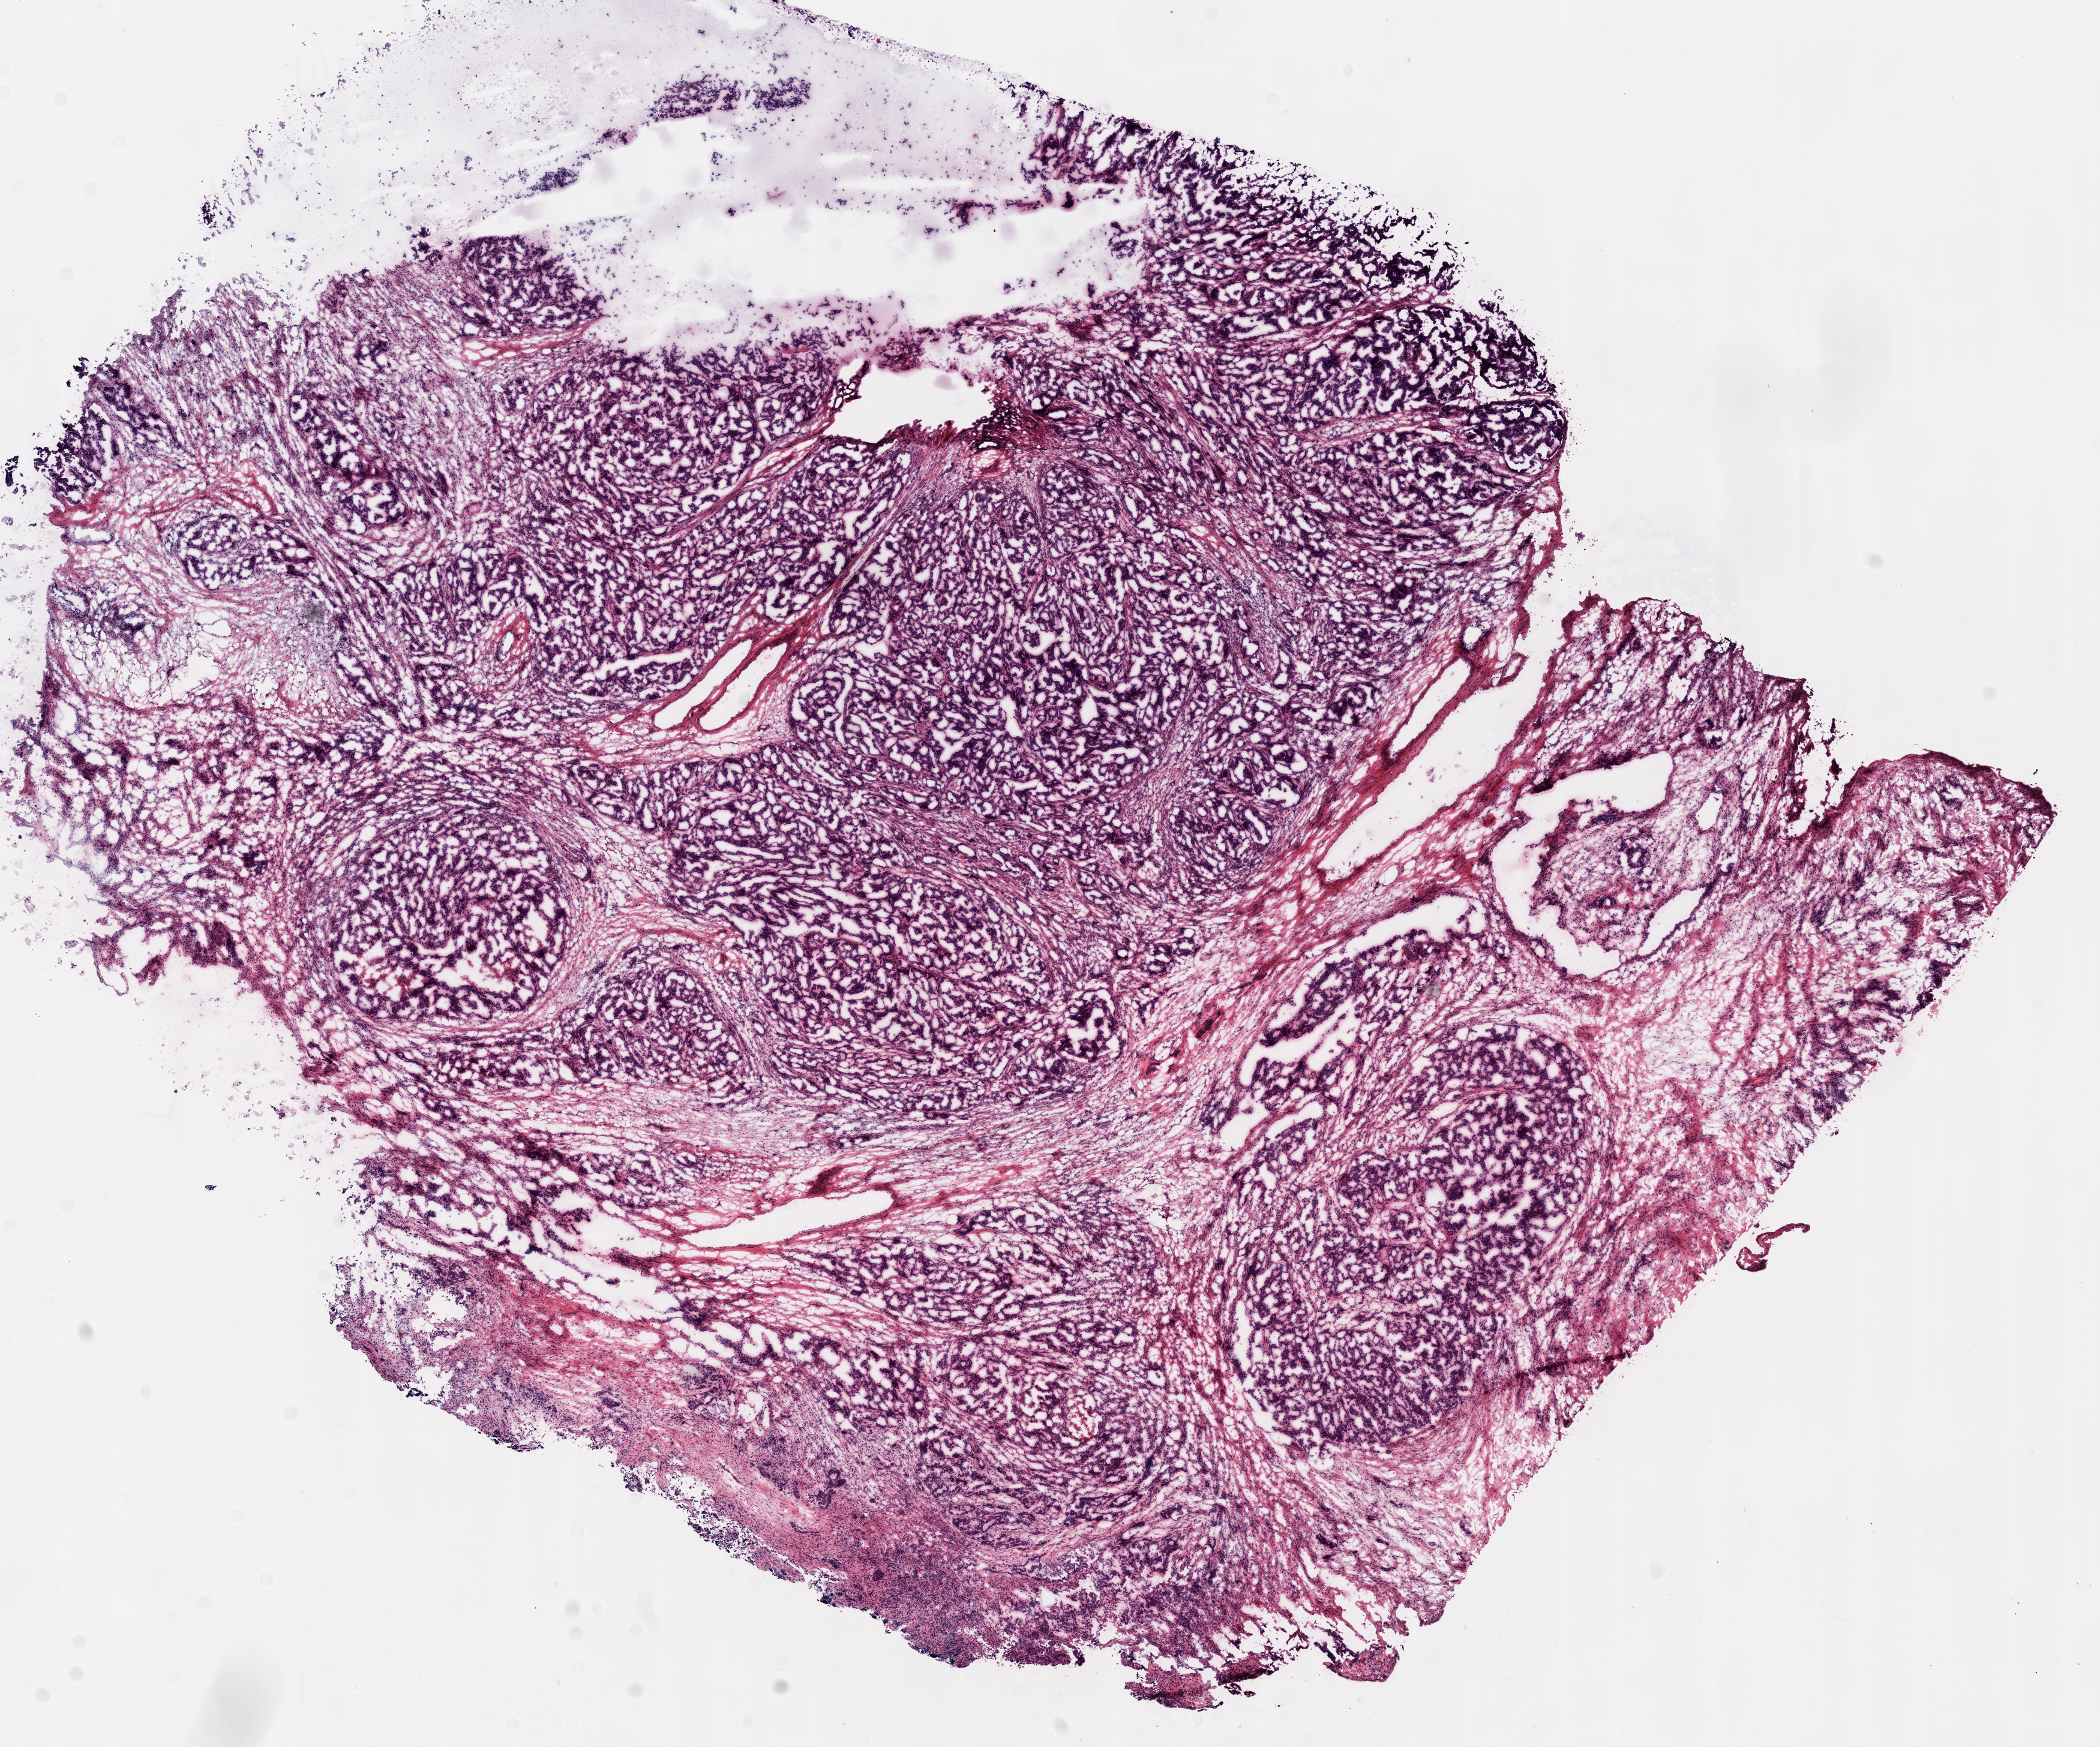
H&E-stained whole-slide image — low-resolution overview of the scanned area, about 14.0 x 11.7 mm, frozen section from the top of the tissue portion, primary tumour sample from the ovary. Female, age 39 years at initial diagnosis. Histologic grade: G3 (poorly differentiated). Composition of this section per pathologist review: tumour cells 89%, tumour nuclei 90%, normal cells 0%, stromal cells 10%, necrosis 1%.
Histologic diagnosis: Serous cystadenocarcinoma, NOS. Laterality: bilateral. FIGO stage: IIIC.